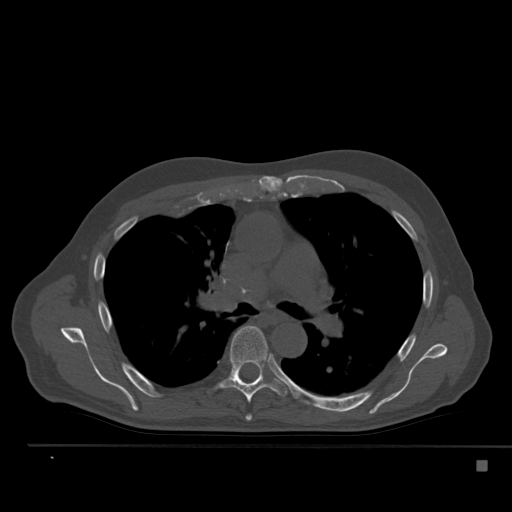
CT including the spine, one axial slice; slice 349 of 517 in the series (ordered by position); reconstruction kernel Br40s; 120 kVp; bone window (W 1800 / L 400 HU); 1.5 mm slice thickness; 512 × 512 image matrix, field of view 408 × 408 mm. Patient: male, 70 years. From the clinical record (not read from this slice): primary cancer: renal.
Annotated regions visible in this slice (semi-automatically segmented with operator editing):
- T5 vertebra: bounding box [x1, y1, x2, y2] px = [246, 414, 252, 421]
- T6 vertebra: [212, 326, 288, 403]